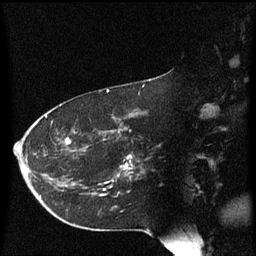
Breast MRI (dynamic contrast-enhanced), one sagittal slice. Position 36 of 60 along the scan axis. Dynamic contrast-enhanced series, image 2 of 3 at this slice position (ordered by acquisition). 1.5 T. TE 4.2 ms, TR 8.4 ms. 2 mm slice thickness. 256 × 256 image matrix. Patient: female, 54 years. From the clinical record (not read from this slice): setting: breast cancer imaged before/during neoadjuvant chemotherapy; receptor status: HR-positive, HER2-negative.
Structures marked on this image (semi-automatically segmented with operator editing):
- analysis volume of interest (the breast-tissue region the enhancement analysis was run in; not a lesion): bounding box [x1, y1, x2, y2] px = [103, 130, 137, 193]
- tumour enhancement mask (voxels above the 70 % enhancement threshold inside the analysis volume of interest): [126, 166, 129, 169]